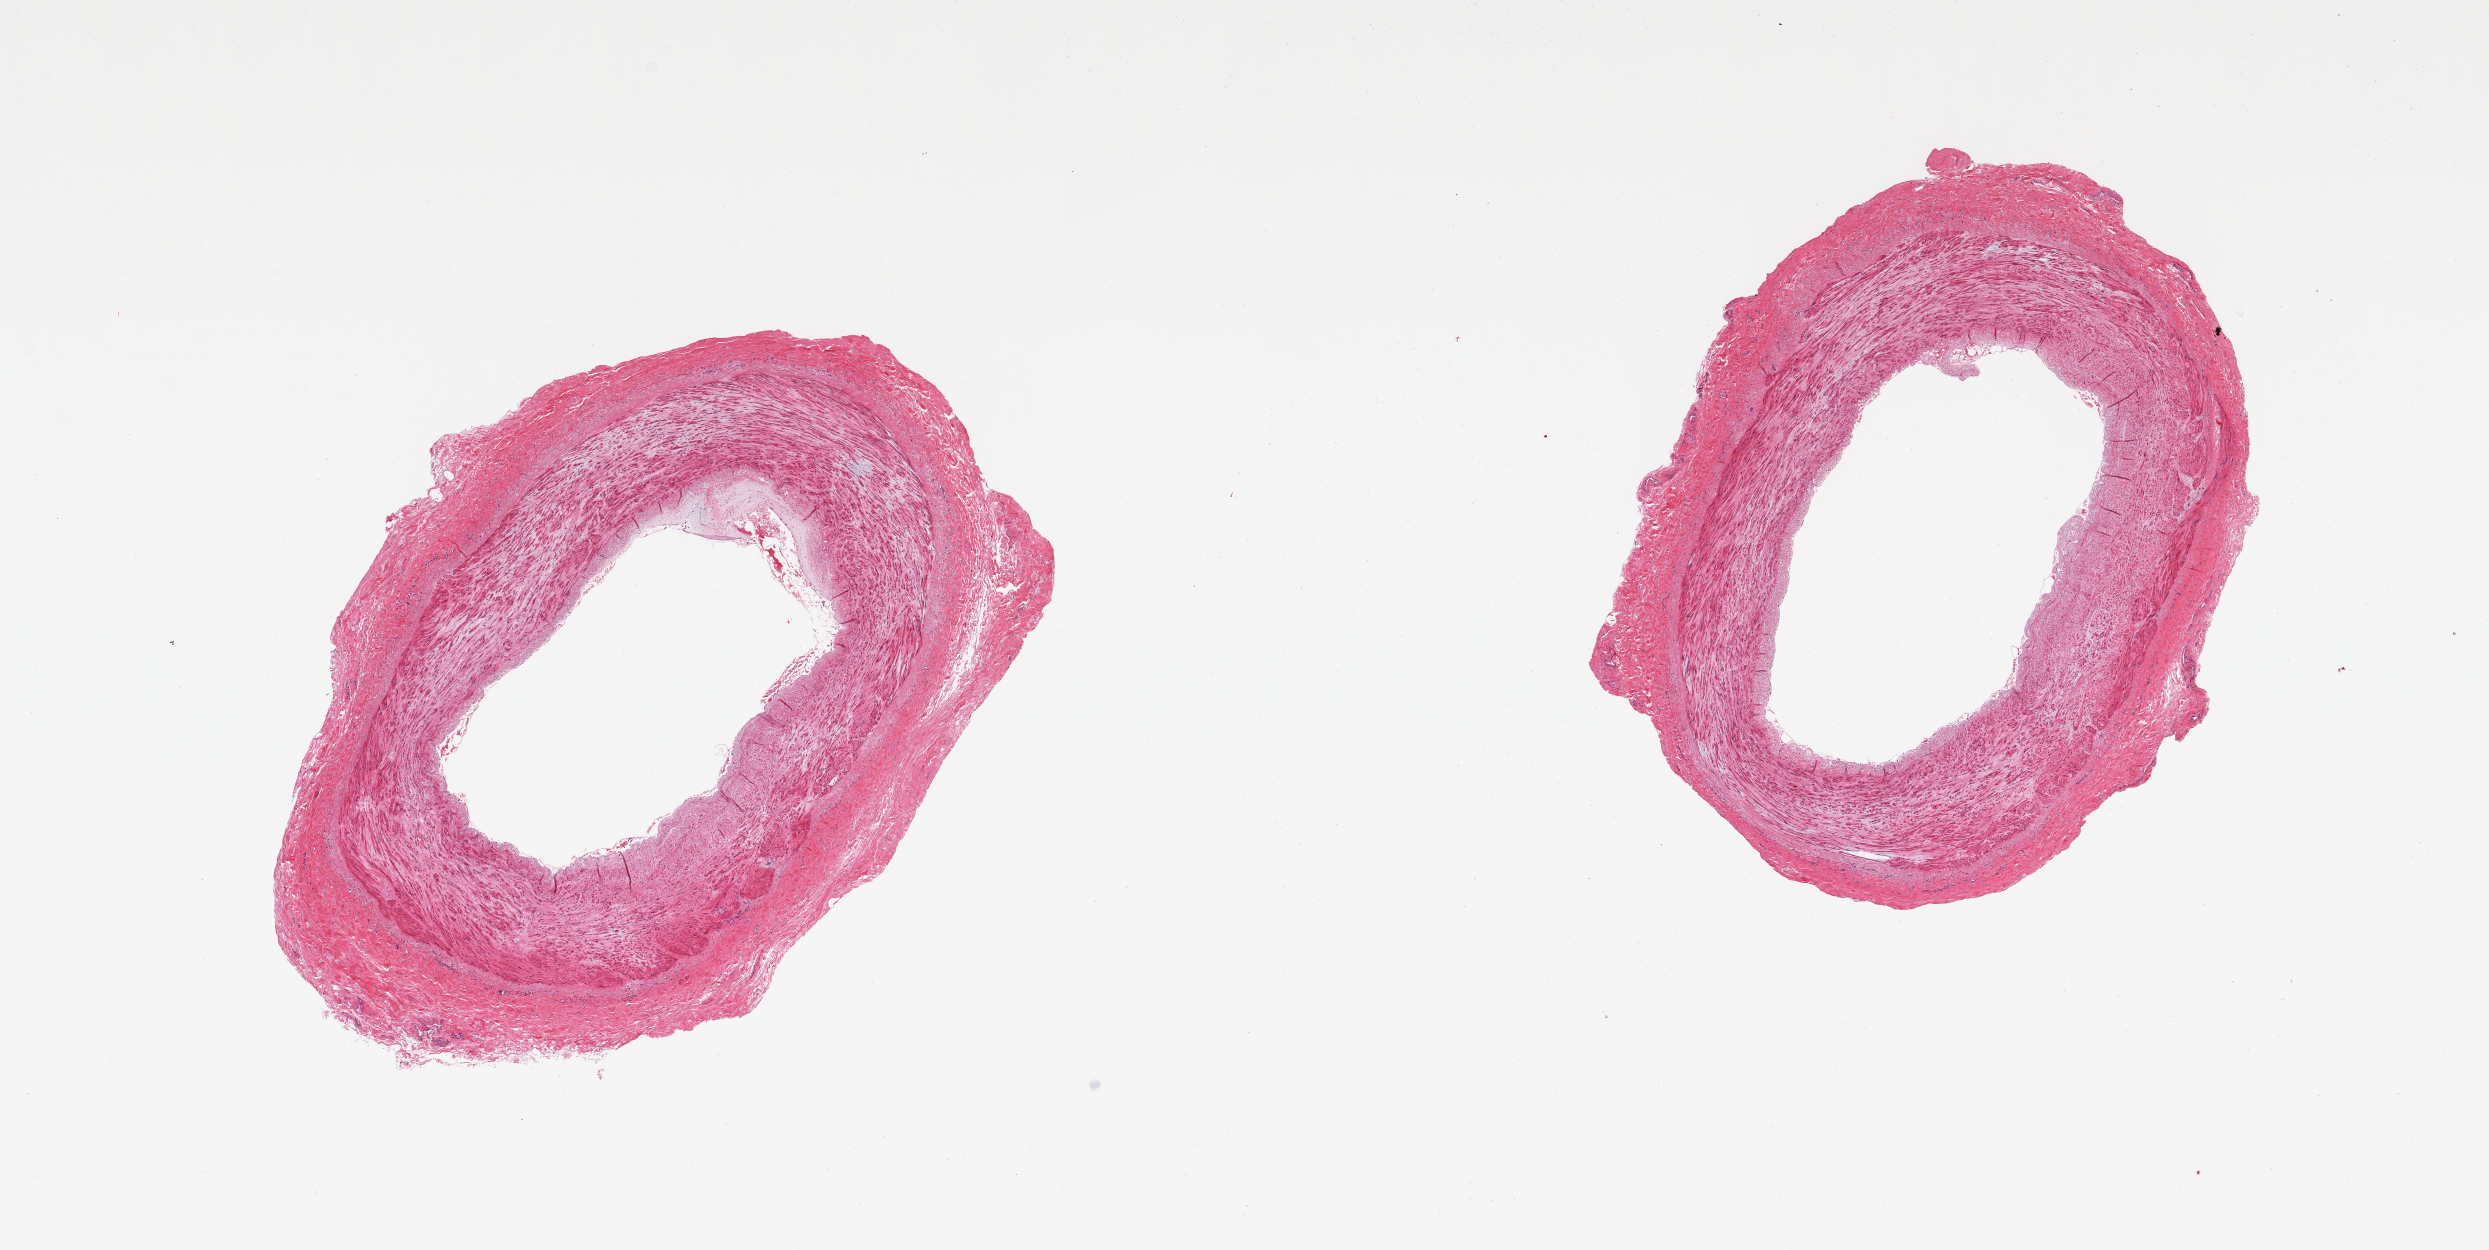
Digitized haematoxylin and eosin-stained section — a low-resolution overview of the entire scanned area, about 19.7 x 9.9 mm. PAXgene-fixed, paraffin-embedded tissue. Sampled site (target tissue): tibial artery. Donor tissue sample. Donor sex: female.
* reviewer comment on this tissue sample: 2 pieces; mild atherosclerosis